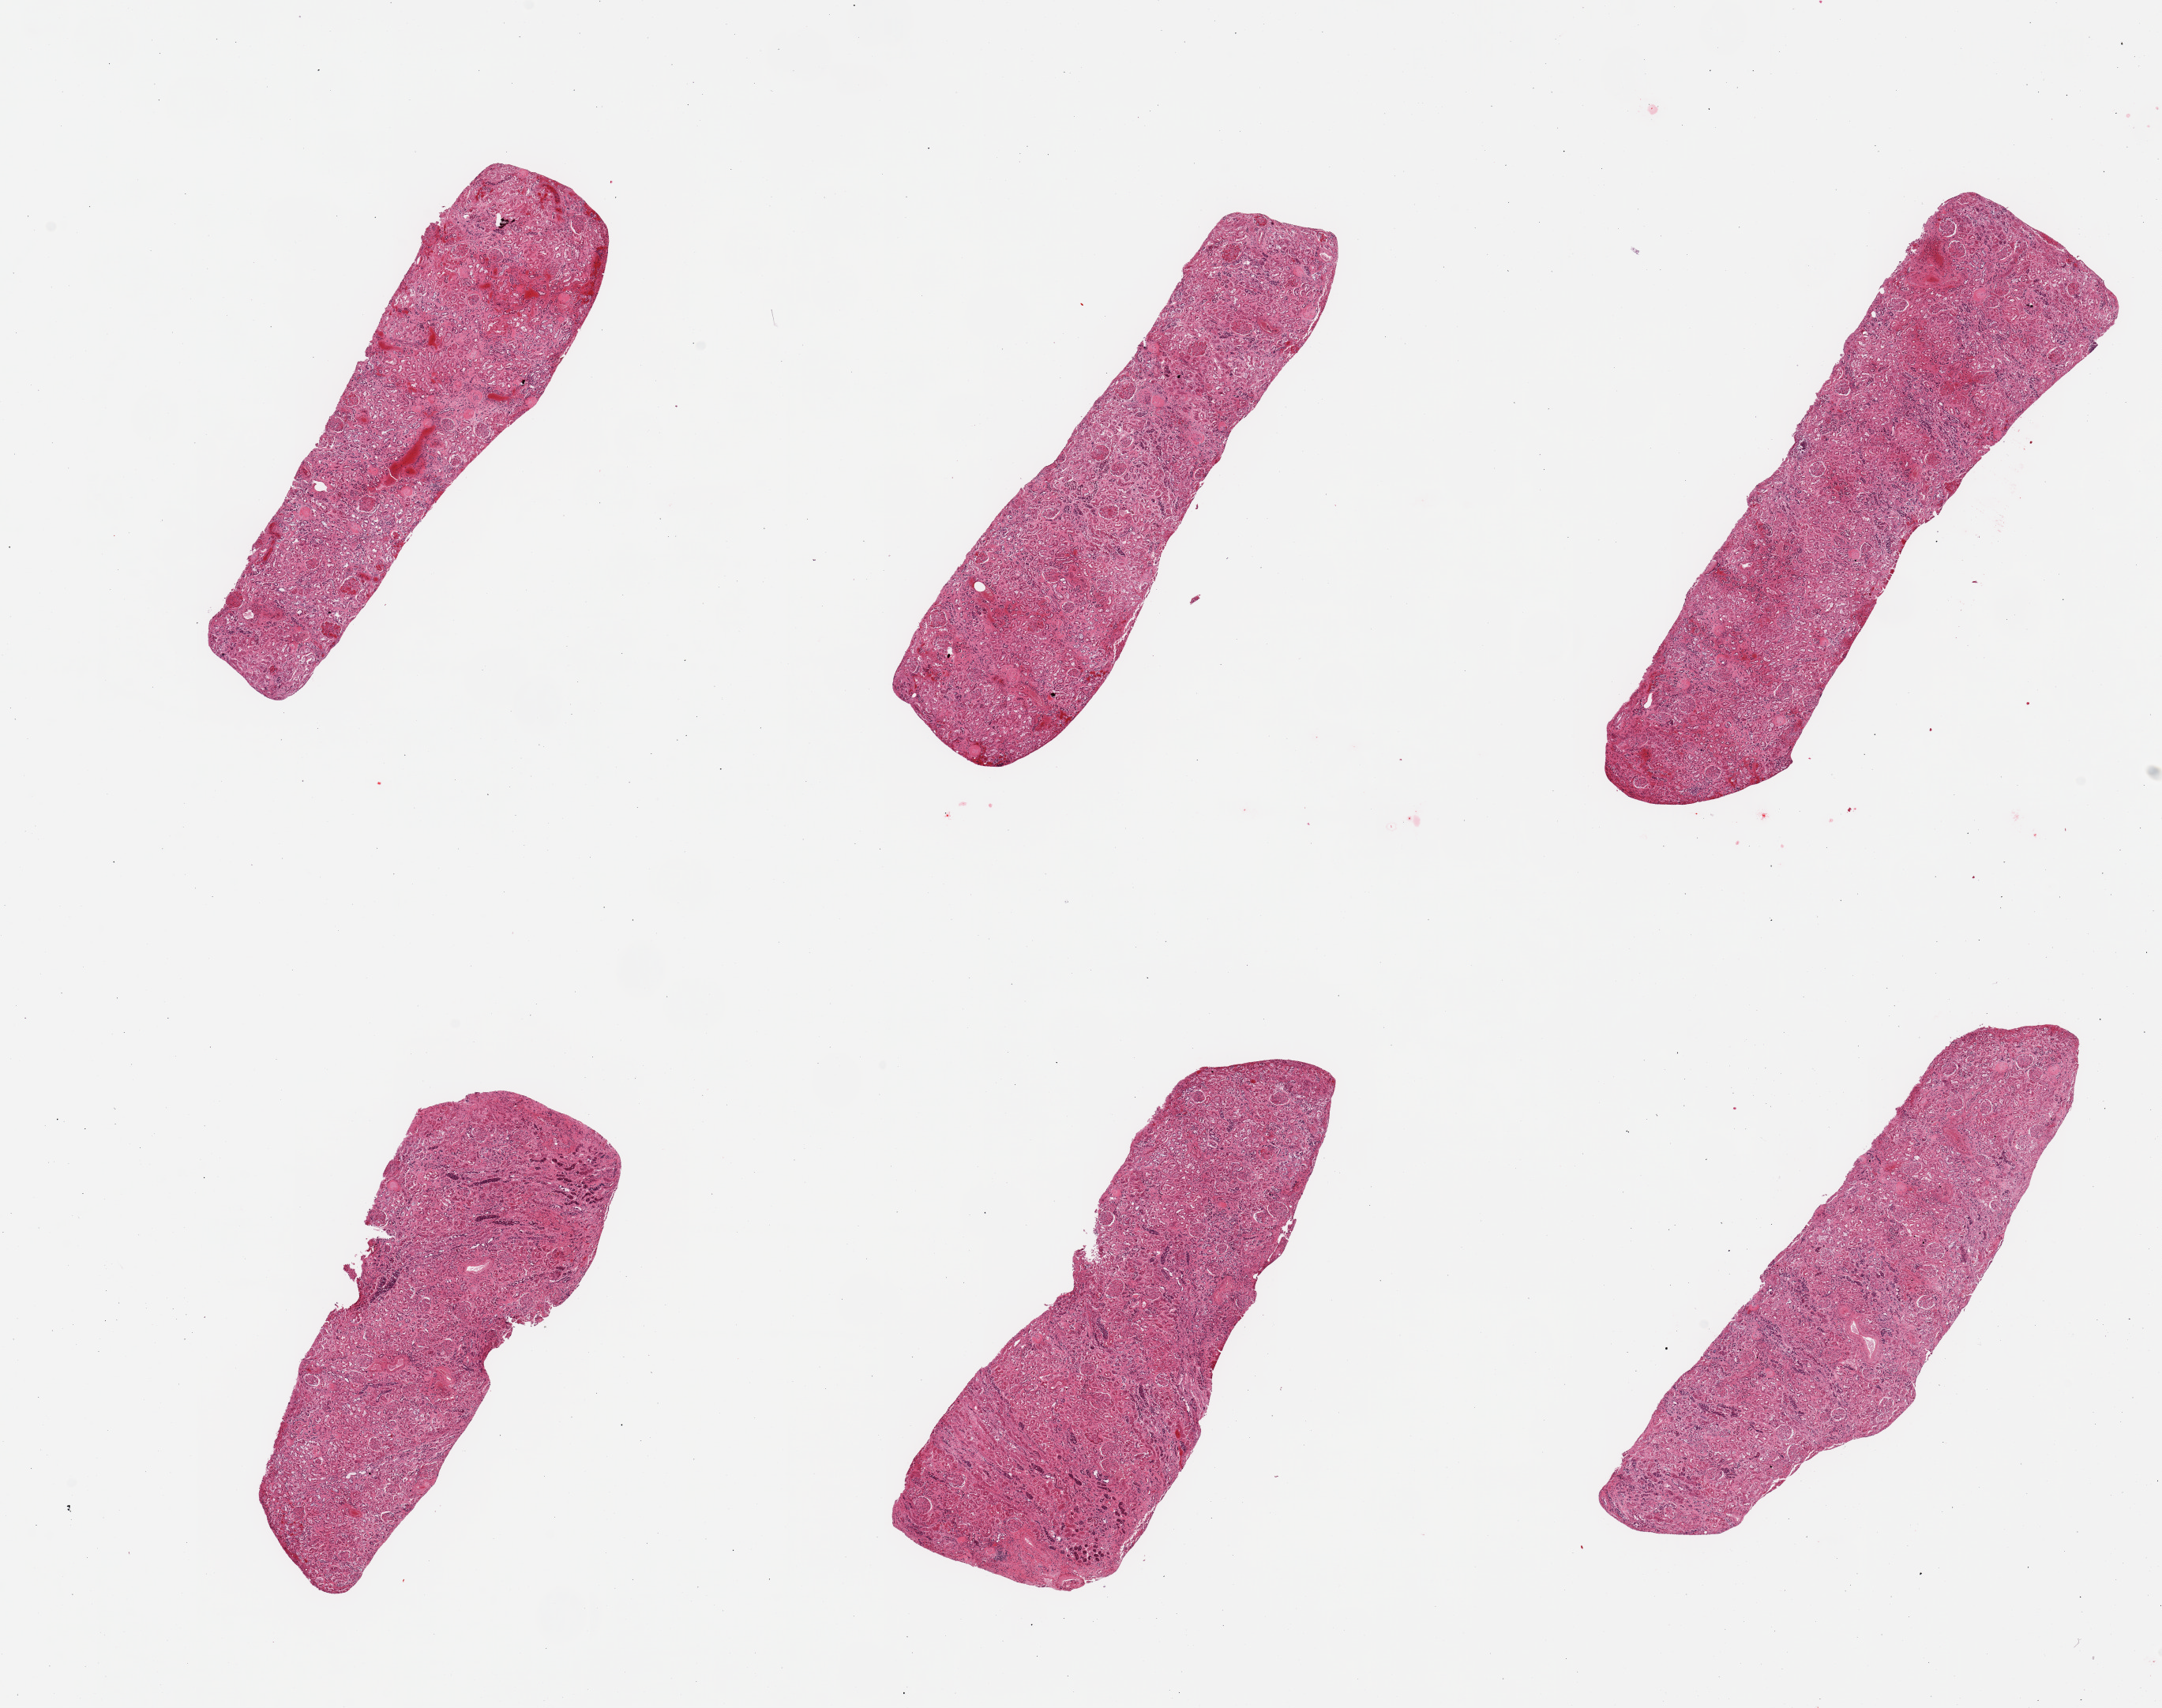
Whole-slide image, hematoxylin and eosin (H&E) stain, brightfield — whole scanned area (about 21.7 x 17.1 mm, acquisition: 20x scan) shown as a low-resolution overview; PAXgene-fixed paraffin-embedded (PFPE) section; sampled site (target tissue): renal cortex; tissue donor sample. Donor: female.
Pathologist's review note for this sample: 6 pieces; 10% sclerosed glomeruli; tubules severely autolyzed.